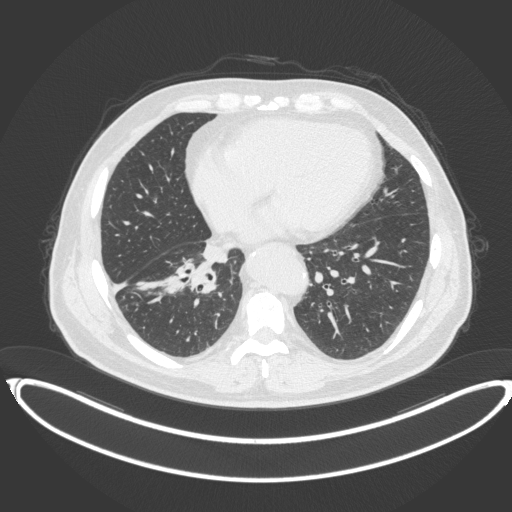
Chest CT, one axial slice; slice 153 of 383 in the series (ordered by position); 120 kVp; lung window (W 1500 / L -600 HU); 1 mm slice thickness; 512 × 512 image matrix, field of view 448 × 448 mm. Patient: male, 61 years. From the clinical record (not read from this slice): clinical TNM (as recorded): T1b N1 M0.
Outlined on this slice (bounding box drawn by a radiologist):
- lung tumour (recorded histology: squamous cell carcinoma): box from (x=163, y=257) to (x=218, y=297) px